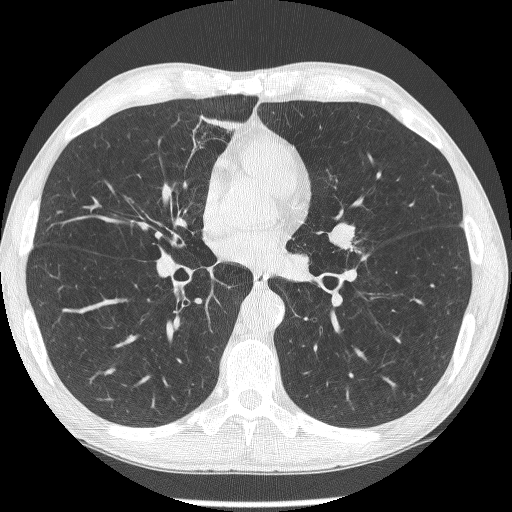
Chest CT (low-dose screening protocol), one axial image; second screening round (one year after baseline); lung window (W 1500 / L -600 HU); 1.25 mm slice thickness; 120 kVp; slice 135 of 293 in the series. Male, age 62 years at enrolment. Former smoker at enrolment.
Lesion marked by an expert reader, bounding box (x1, y1, x2, y2) in pixels: (320, 217, 369, 265). The screening reader recorded 2 non-calcified nodules or masses ≥4 mm on this exam (lingula, lingula); which of them this box marks is not recorded. Later outcome: lung cancer diagnosed 95 days after this screen — small cell carcinoma, NOS, left upper lobe, stage IIIA (AJCC 6th edition).